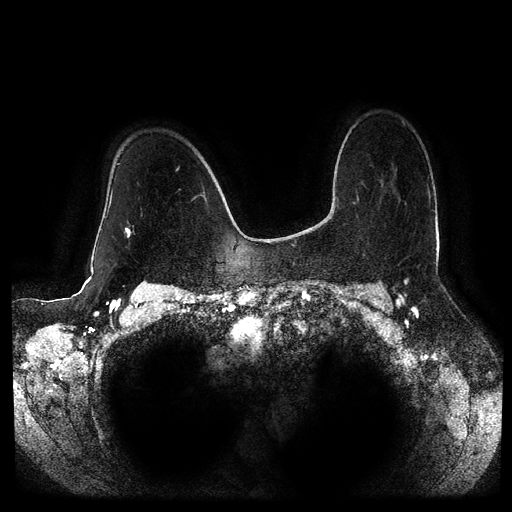
Breast MRI (dynamic contrast-enhanced, multi-phase), one axial slice; position 73 of 116 along the scan axis; dynamic contrast-enhanced series, time point 2 of 5 at this slice position (early post-contrast); 1.5 T; TE 2.6 ms, TR 5.2 ms; 2 mm slice thickness; 512 × 512 image matrix, field of view 380 × 380 mm. Female patient, age 53 years.
Structures marked on this image (semi-automatic segmentation, software-assisted and operator-edited):
- breast lesion (labelled 'tumour' in the annotation; benign lesions carry a separate 'benign' label): bounding box <124,227,132,238> (left, top, right, bottom; pixels)